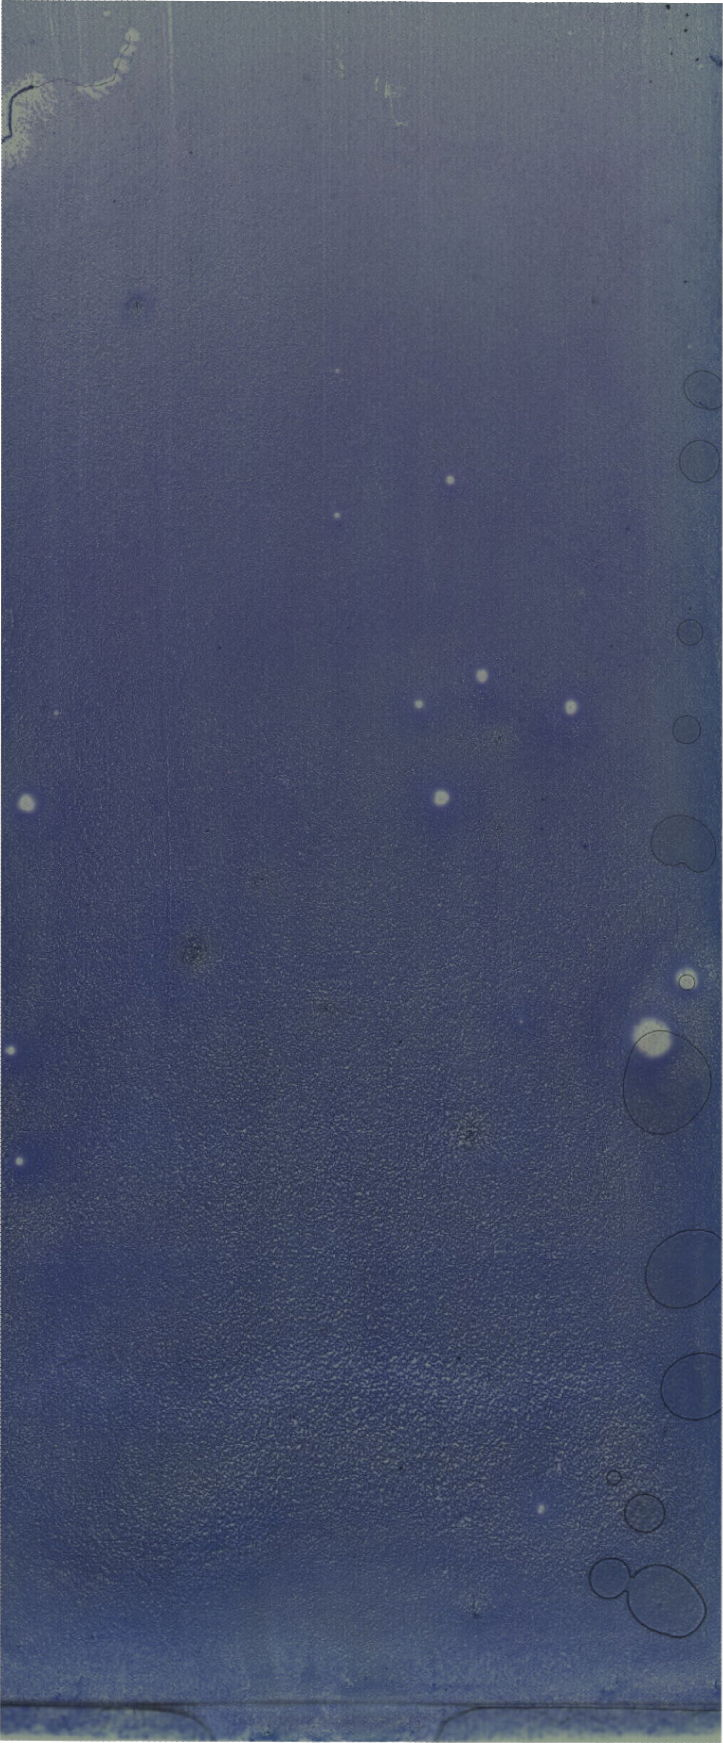
May-Grünwald-Giemsa (MGG)-stained marrow aspirate smear (whole slide), shown as a low-resolution overview of the whole scanned area (about 20.5 x 49.4 mm). Patient sex: female.
Diagnosis: Acute Myeloid Leukemia with Maturation.